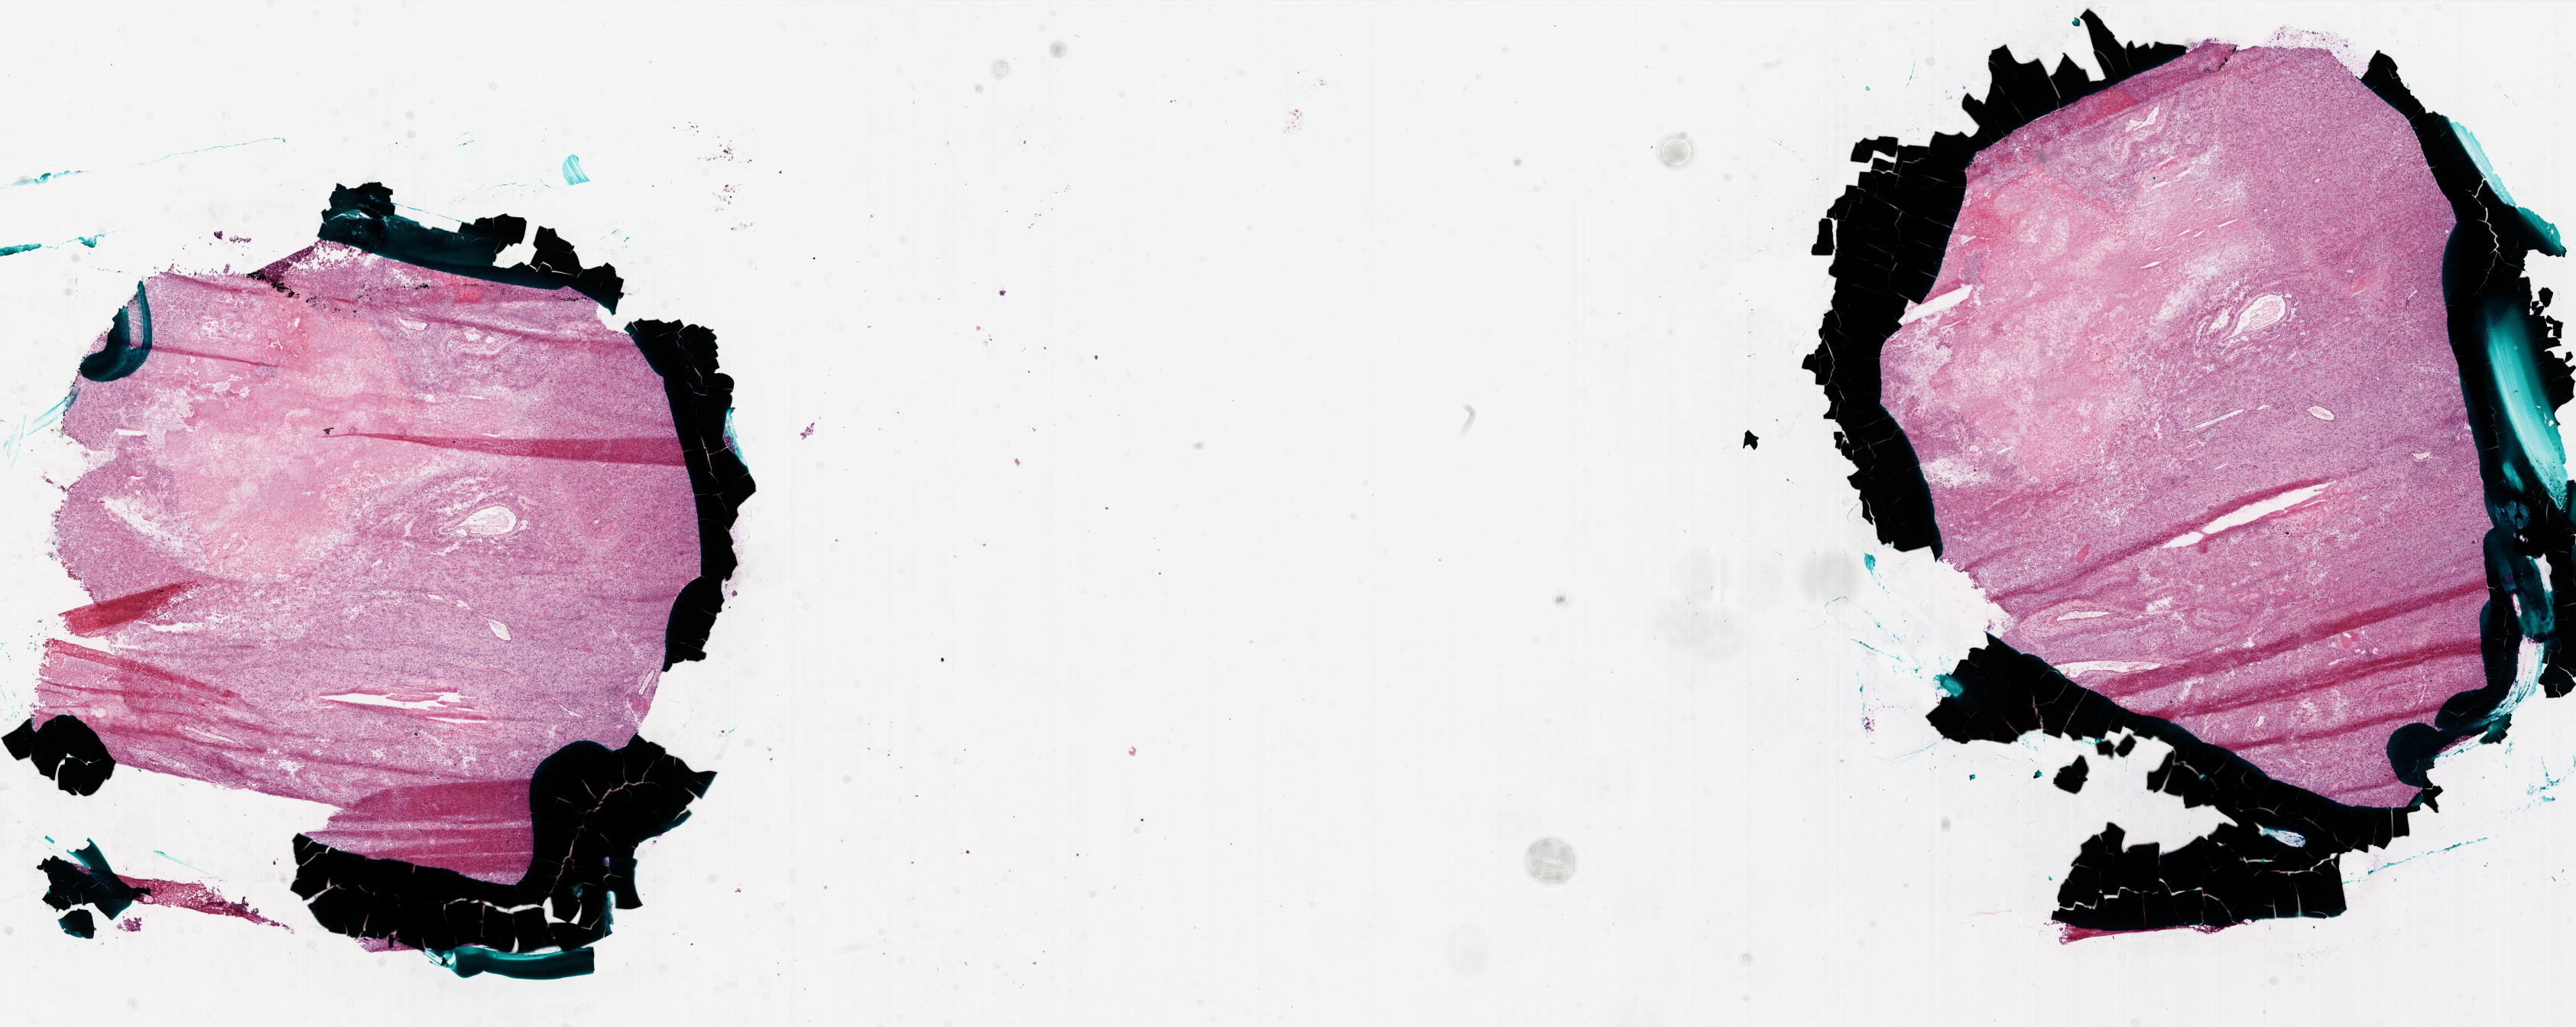
Digitized Hematoxylin and eosin (H&E) stained tissue section (whole slide), shown as a low-resolution overview of the whole scanned area (about 27.0 x 10.7 mm, from a 20x scan); frozen section; primary tumour sample from the brain. Female, age 74 years at initial diagnosis. Composition of this section per pathologist review: tumour cells 75%, tumour nuclei 100%.
Pathologic diagnosis: Glioblastoma.